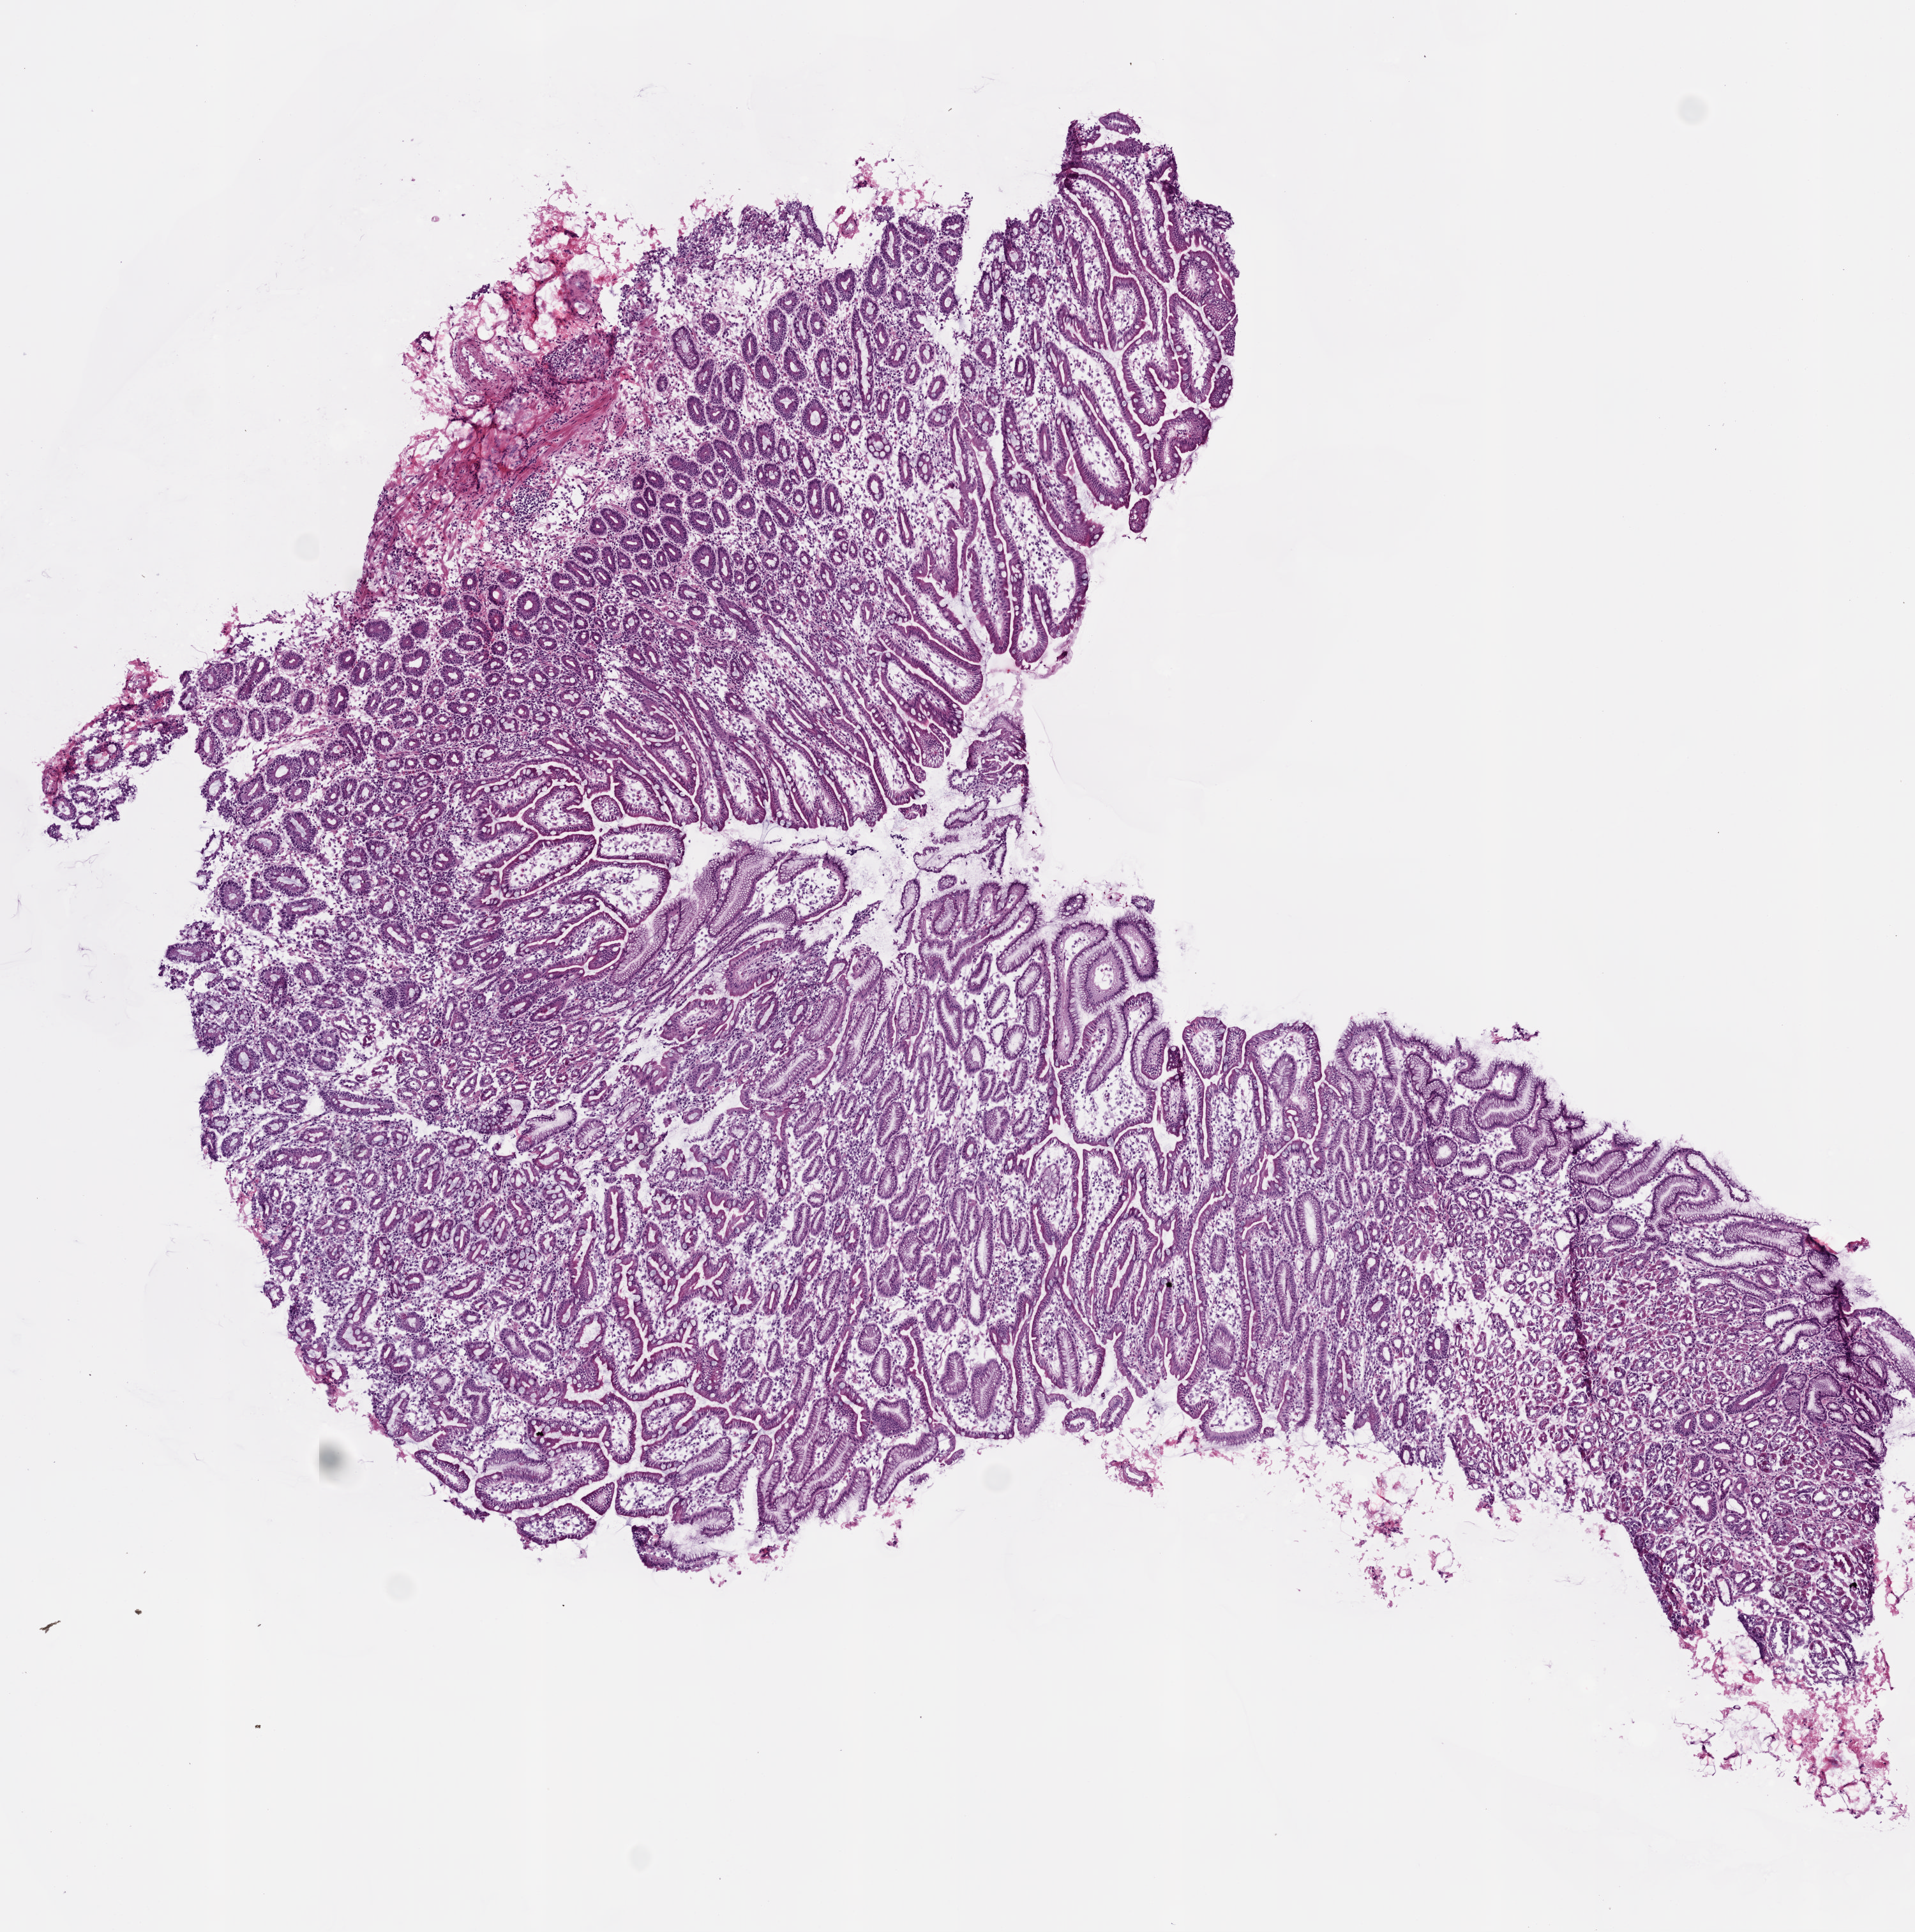
Hematoxylin and eosin (H&E) stained whole-slide image, shown as a low-resolution overview of the whole scanned area (about 6.0 x 6.1 mm, acquisition: 20x scan). Frozen section from the top of the tissue portion. Sample: solid tissue normal (non-tumour tissue), stomach. Male patient.
• this section: solid tissue normal (non-tumour) sample from the same patient
• patient diagnosis: Adenocarcinoma, NOS (cardia, NOS)